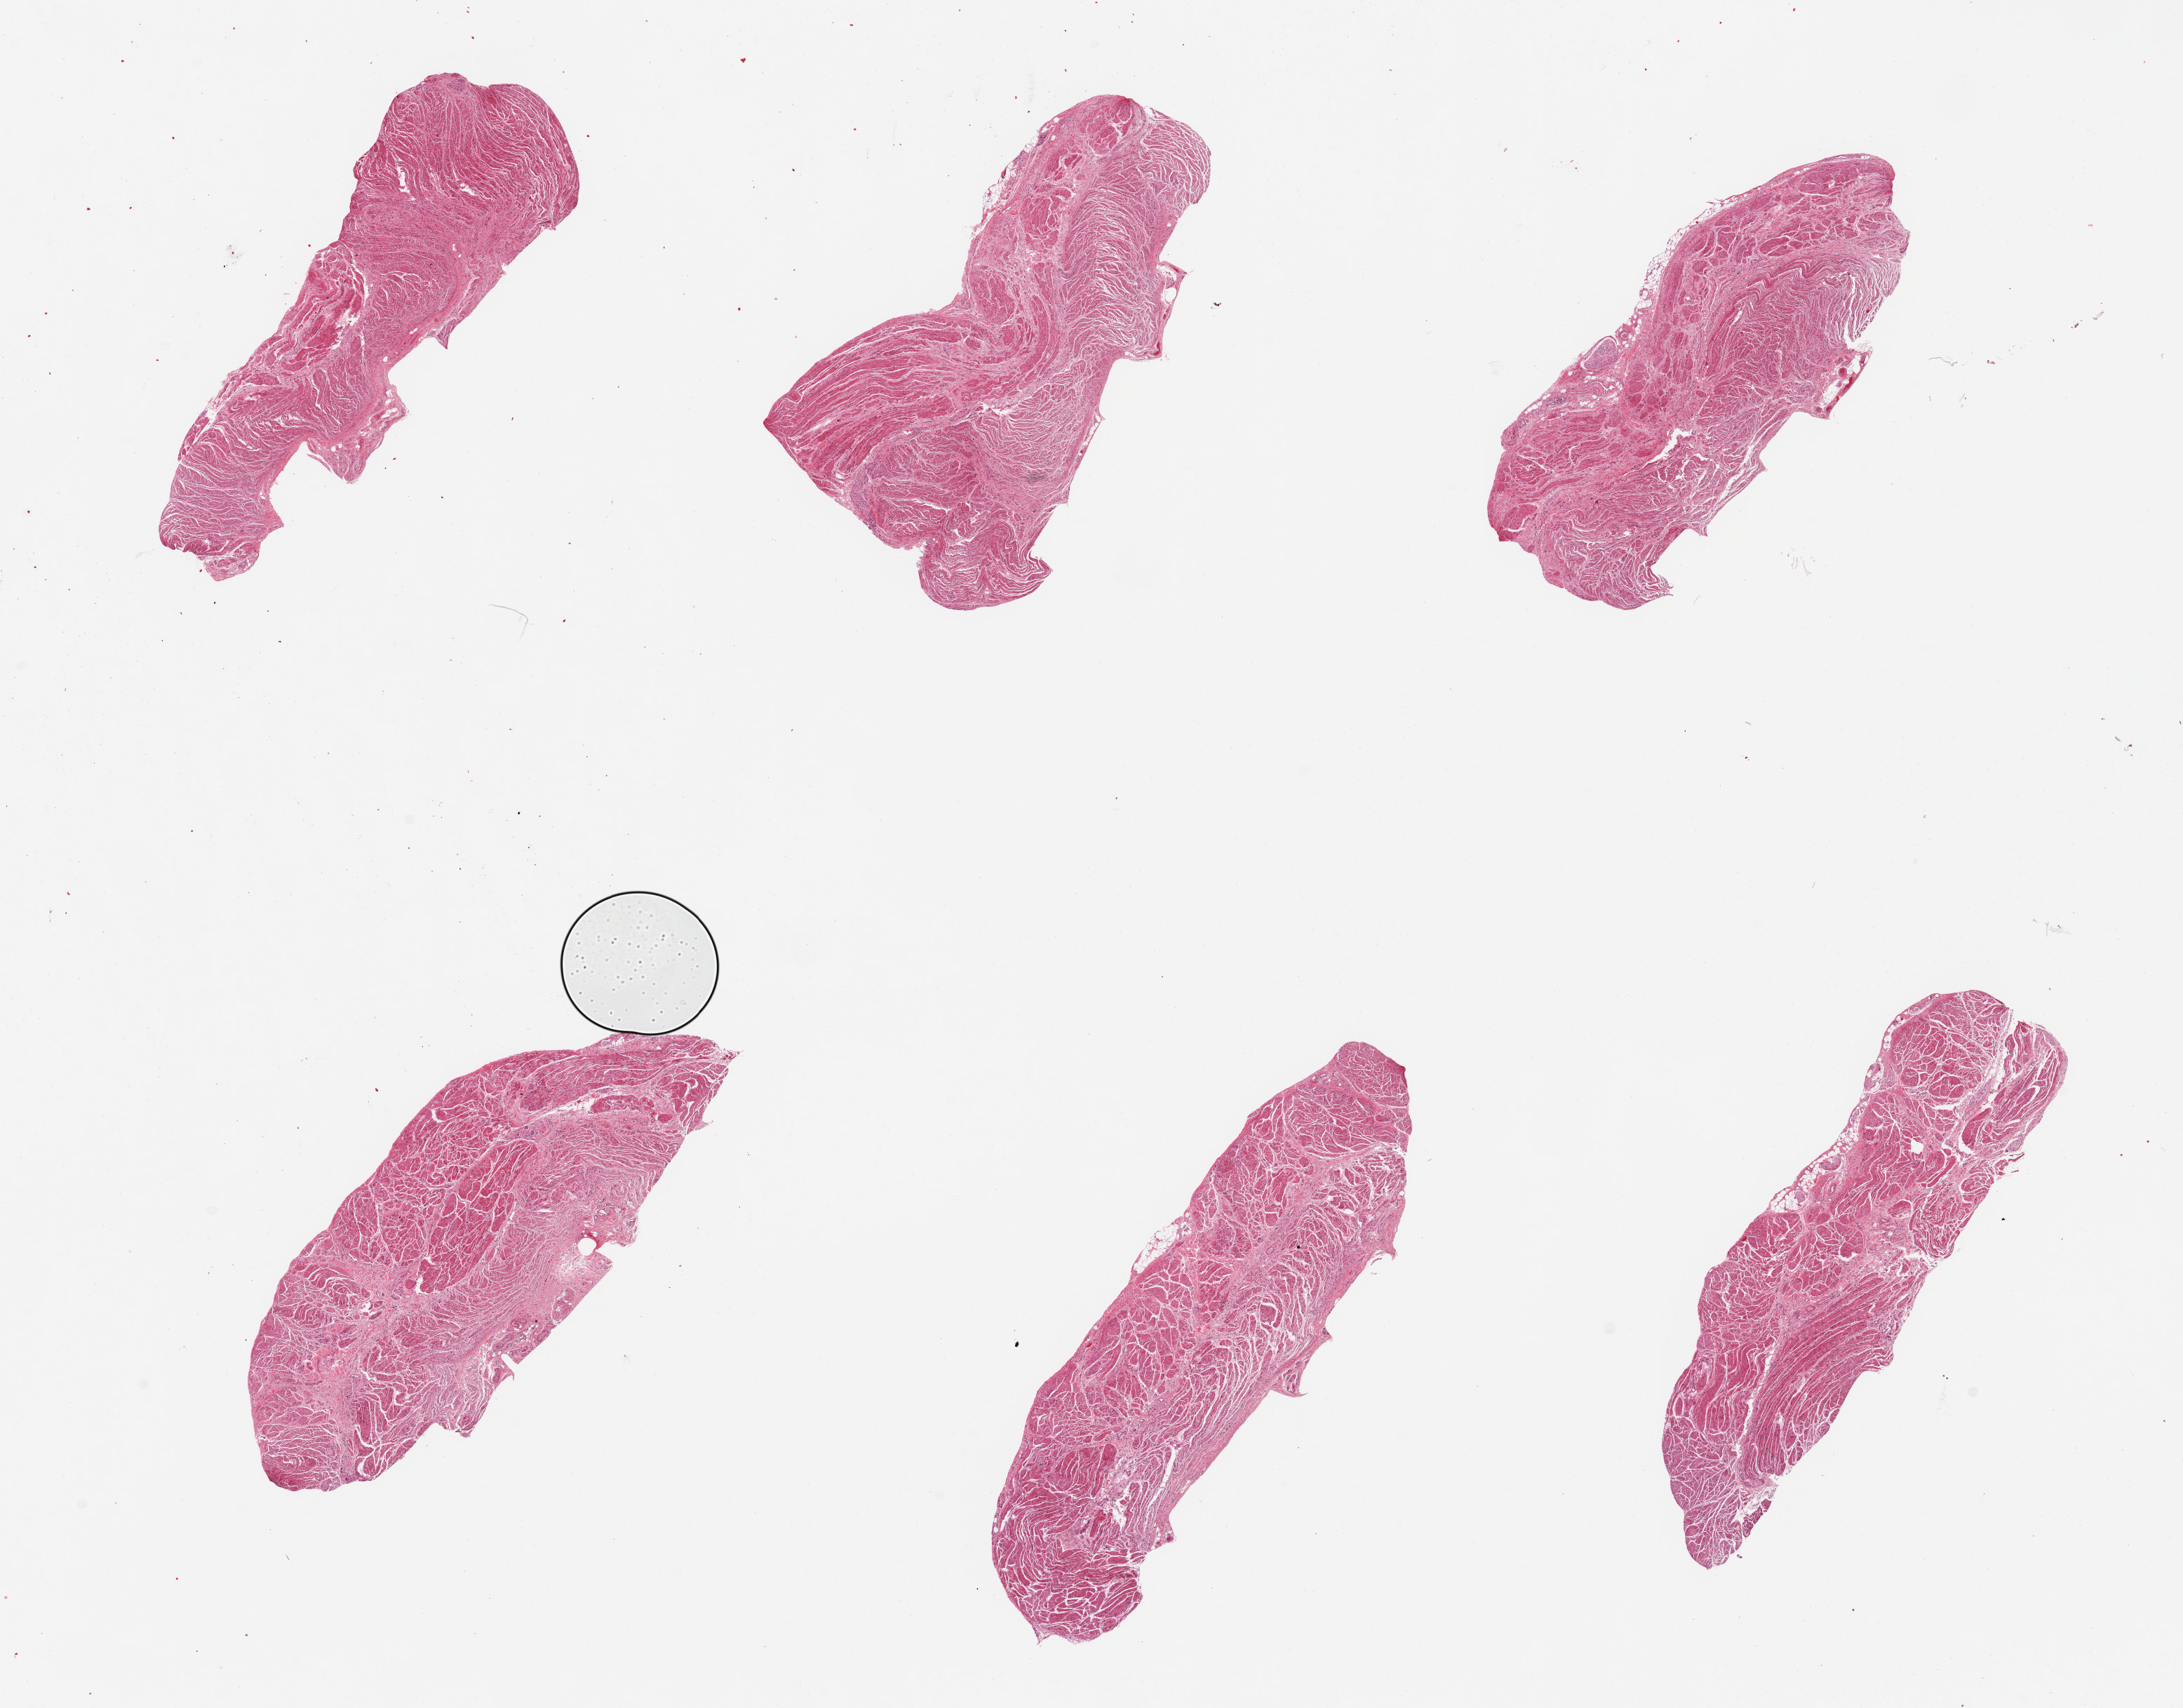
Digitized H&E-stained section — shown as a low-resolution overview of the whole scanned area (about 24.6 x 19.3 mm), PAXgene-fixed, paraffin-embedded tissue, section of gastroesophageal junction (target tissue), donor tissue sample. Donor: female.
Review note (as recorded): pieces.